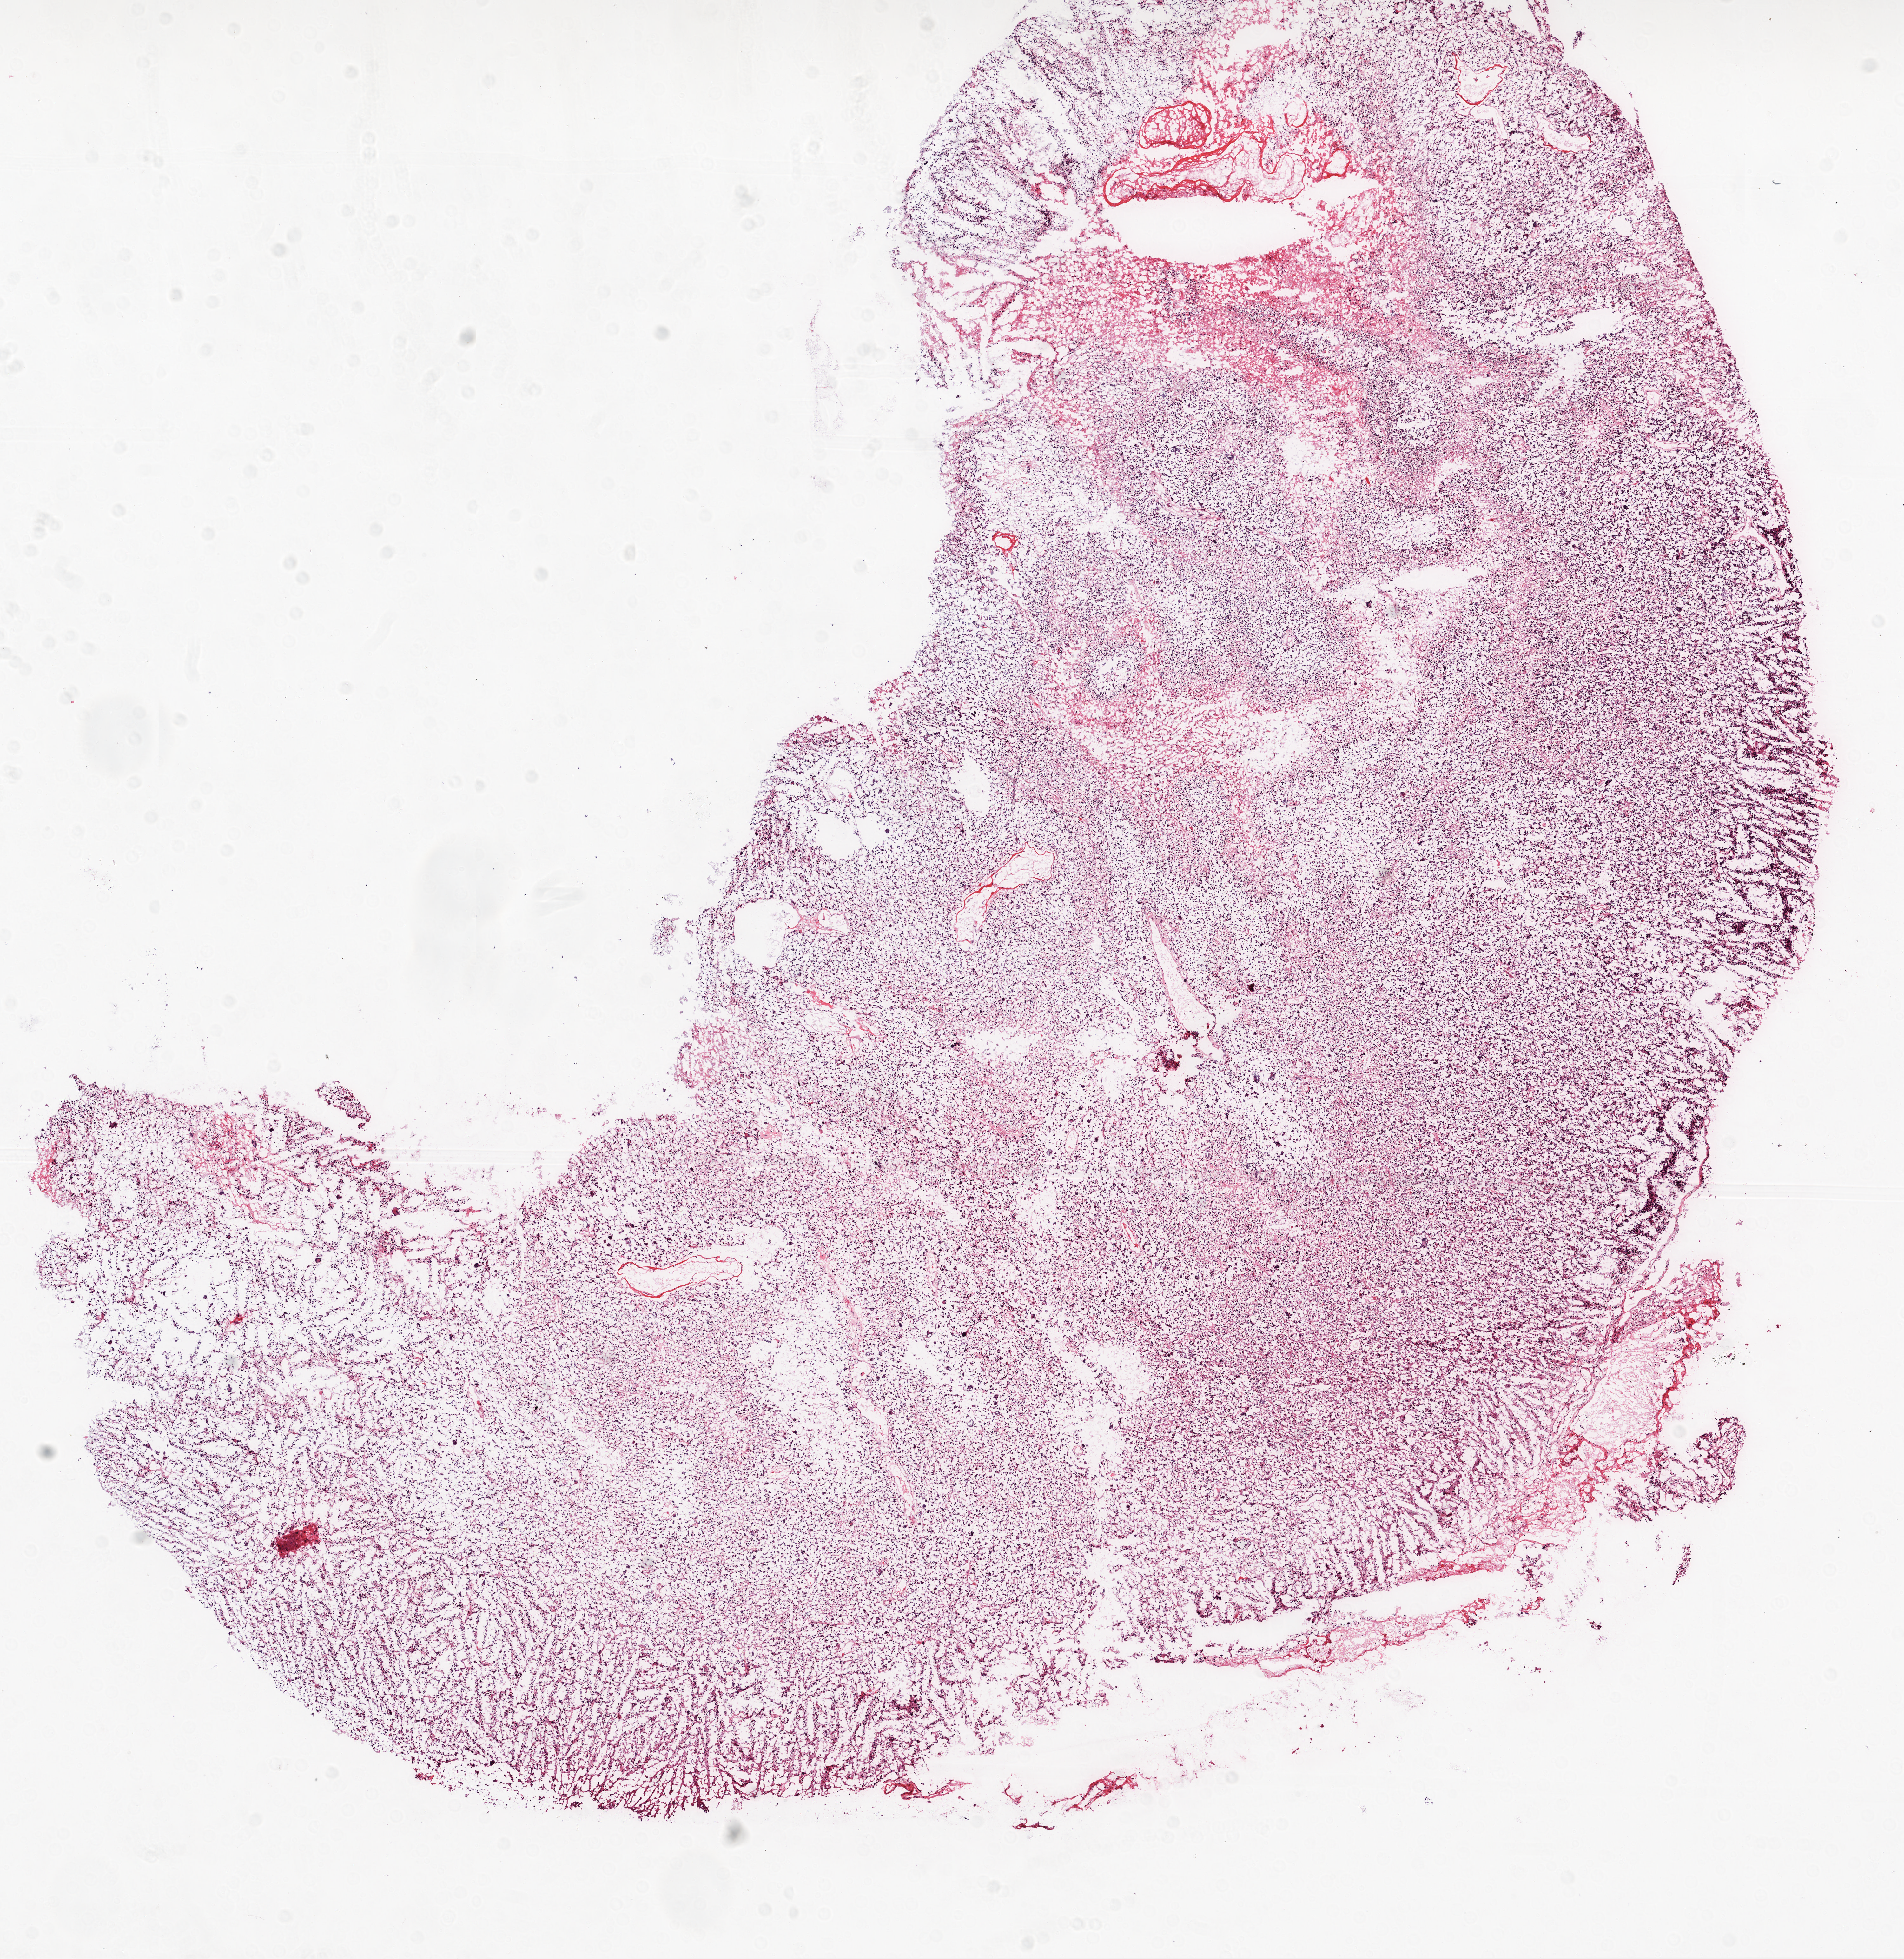
Hematoxylin and eosin (H&E) stained whole-slide image, low-resolution overview of the scanned area, about 12.0 x 12.4 mm. Frozen section from the top of the tissue portion. Recurrent tumour sample from the brain. Female, age 60 years at initial diagnosis. Pathologist review of this section (percent, as recorded): tumour cells 80%, tumour nuclei 90%, normal cells 0%, stromal cells 0%, necrosis 20%.
* this section: recurrent tumour
* patient diagnosis: Glioblastoma